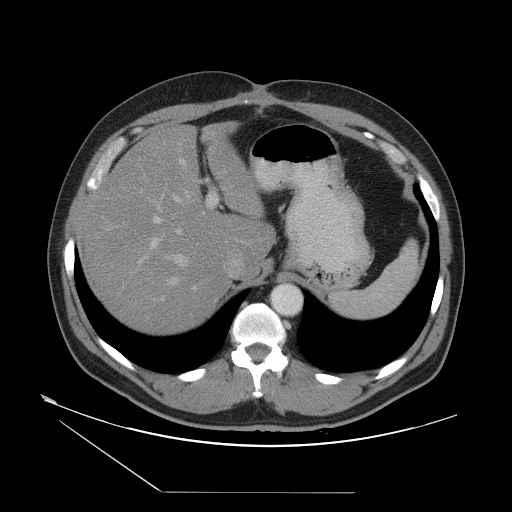
Contrast-enhanced abdominal CT, one axial slice. Position 37 of 55 along the scan axis. 120 kVp. Soft-tissue window (W 400 / L 40 HU). 5 mm slice thickness. 512 × 512 image matrix. Male patient, age 59 years. From the clinical record (not read from this slice): diagnosis: colorectal cancer liver metastases, imaged before liver resection; multiple liver metastases: yes; largest metastasis: 0.3 cm; chemotherapy before resection: yes.
Annotated regions visible in this slice (expert manual segmentation):
- hepatic veins: bounding box [x1, y1, x2, y2] px = [161, 193, 203, 286]
- liver: [84, 127, 271, 332]
- planned liver remnant (the part of the liver to remain after resection): [84, 149, 271, 333]
- portal vein (with intrahepatic branches): [138, 160, 217, 301]